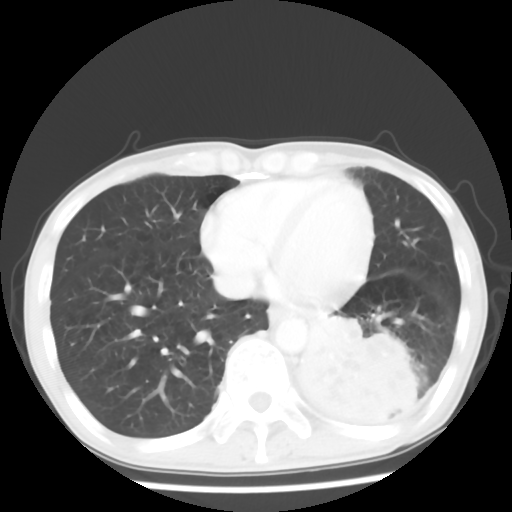
Chest CT, one axial slice; slice 19 of 64 in the series (ordered by position); 120 kVp; lung window (W 1500 / L -600 HU); 5 mm slice thickness; 512 × 512 image matrix. Patient: male, 68 years. Case-level facts recorded for this patient, not image findings: clinical TNM (as recorded): T4 N0 M0.
Outlined on this slice (rectangle marked by the reading radiologist):
- lung tumour (recorded histology: squamous cell carcinoma): bounding box (x1, y1, x2, y2) in pixels: (289, 310, 419, 430)